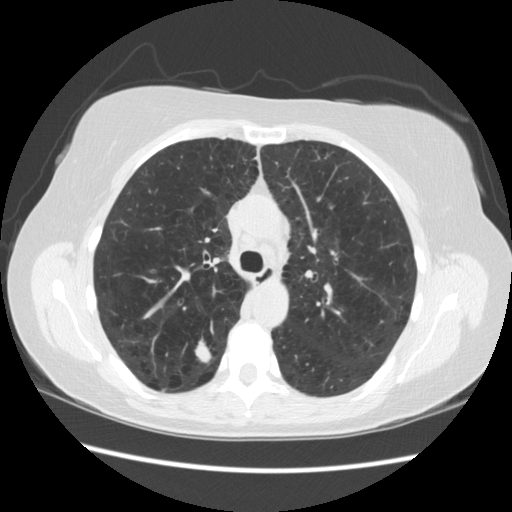
Low-dose screening chest CT, axial slice, third annual screen, lung window (W 1500 / L -600 HU), slice 77 of 235 in the series, 512 × 512 image matrix, field of view 360 × 360 mm. Female participant, aged 55 years at enrolment. Current smoker at enrolment.
Expert reader's lesion annotation, bounding box (x1, y1, x2, y2) in pixels: (178, 329, 228, 375). The exam's reader record, not a measurement of the box and not confirmed to be the same lesion: non-calcified nodule or mass ≥4 mm, right upper lobe, 11 × 11 mm, poorly defined margins, soft tissue attenuation, pre-existing on the prior screen: no. Participant outcome: lung cancer diagnosed 96 days after this screen — small cell carcinoma, NOS, right upper lobe.